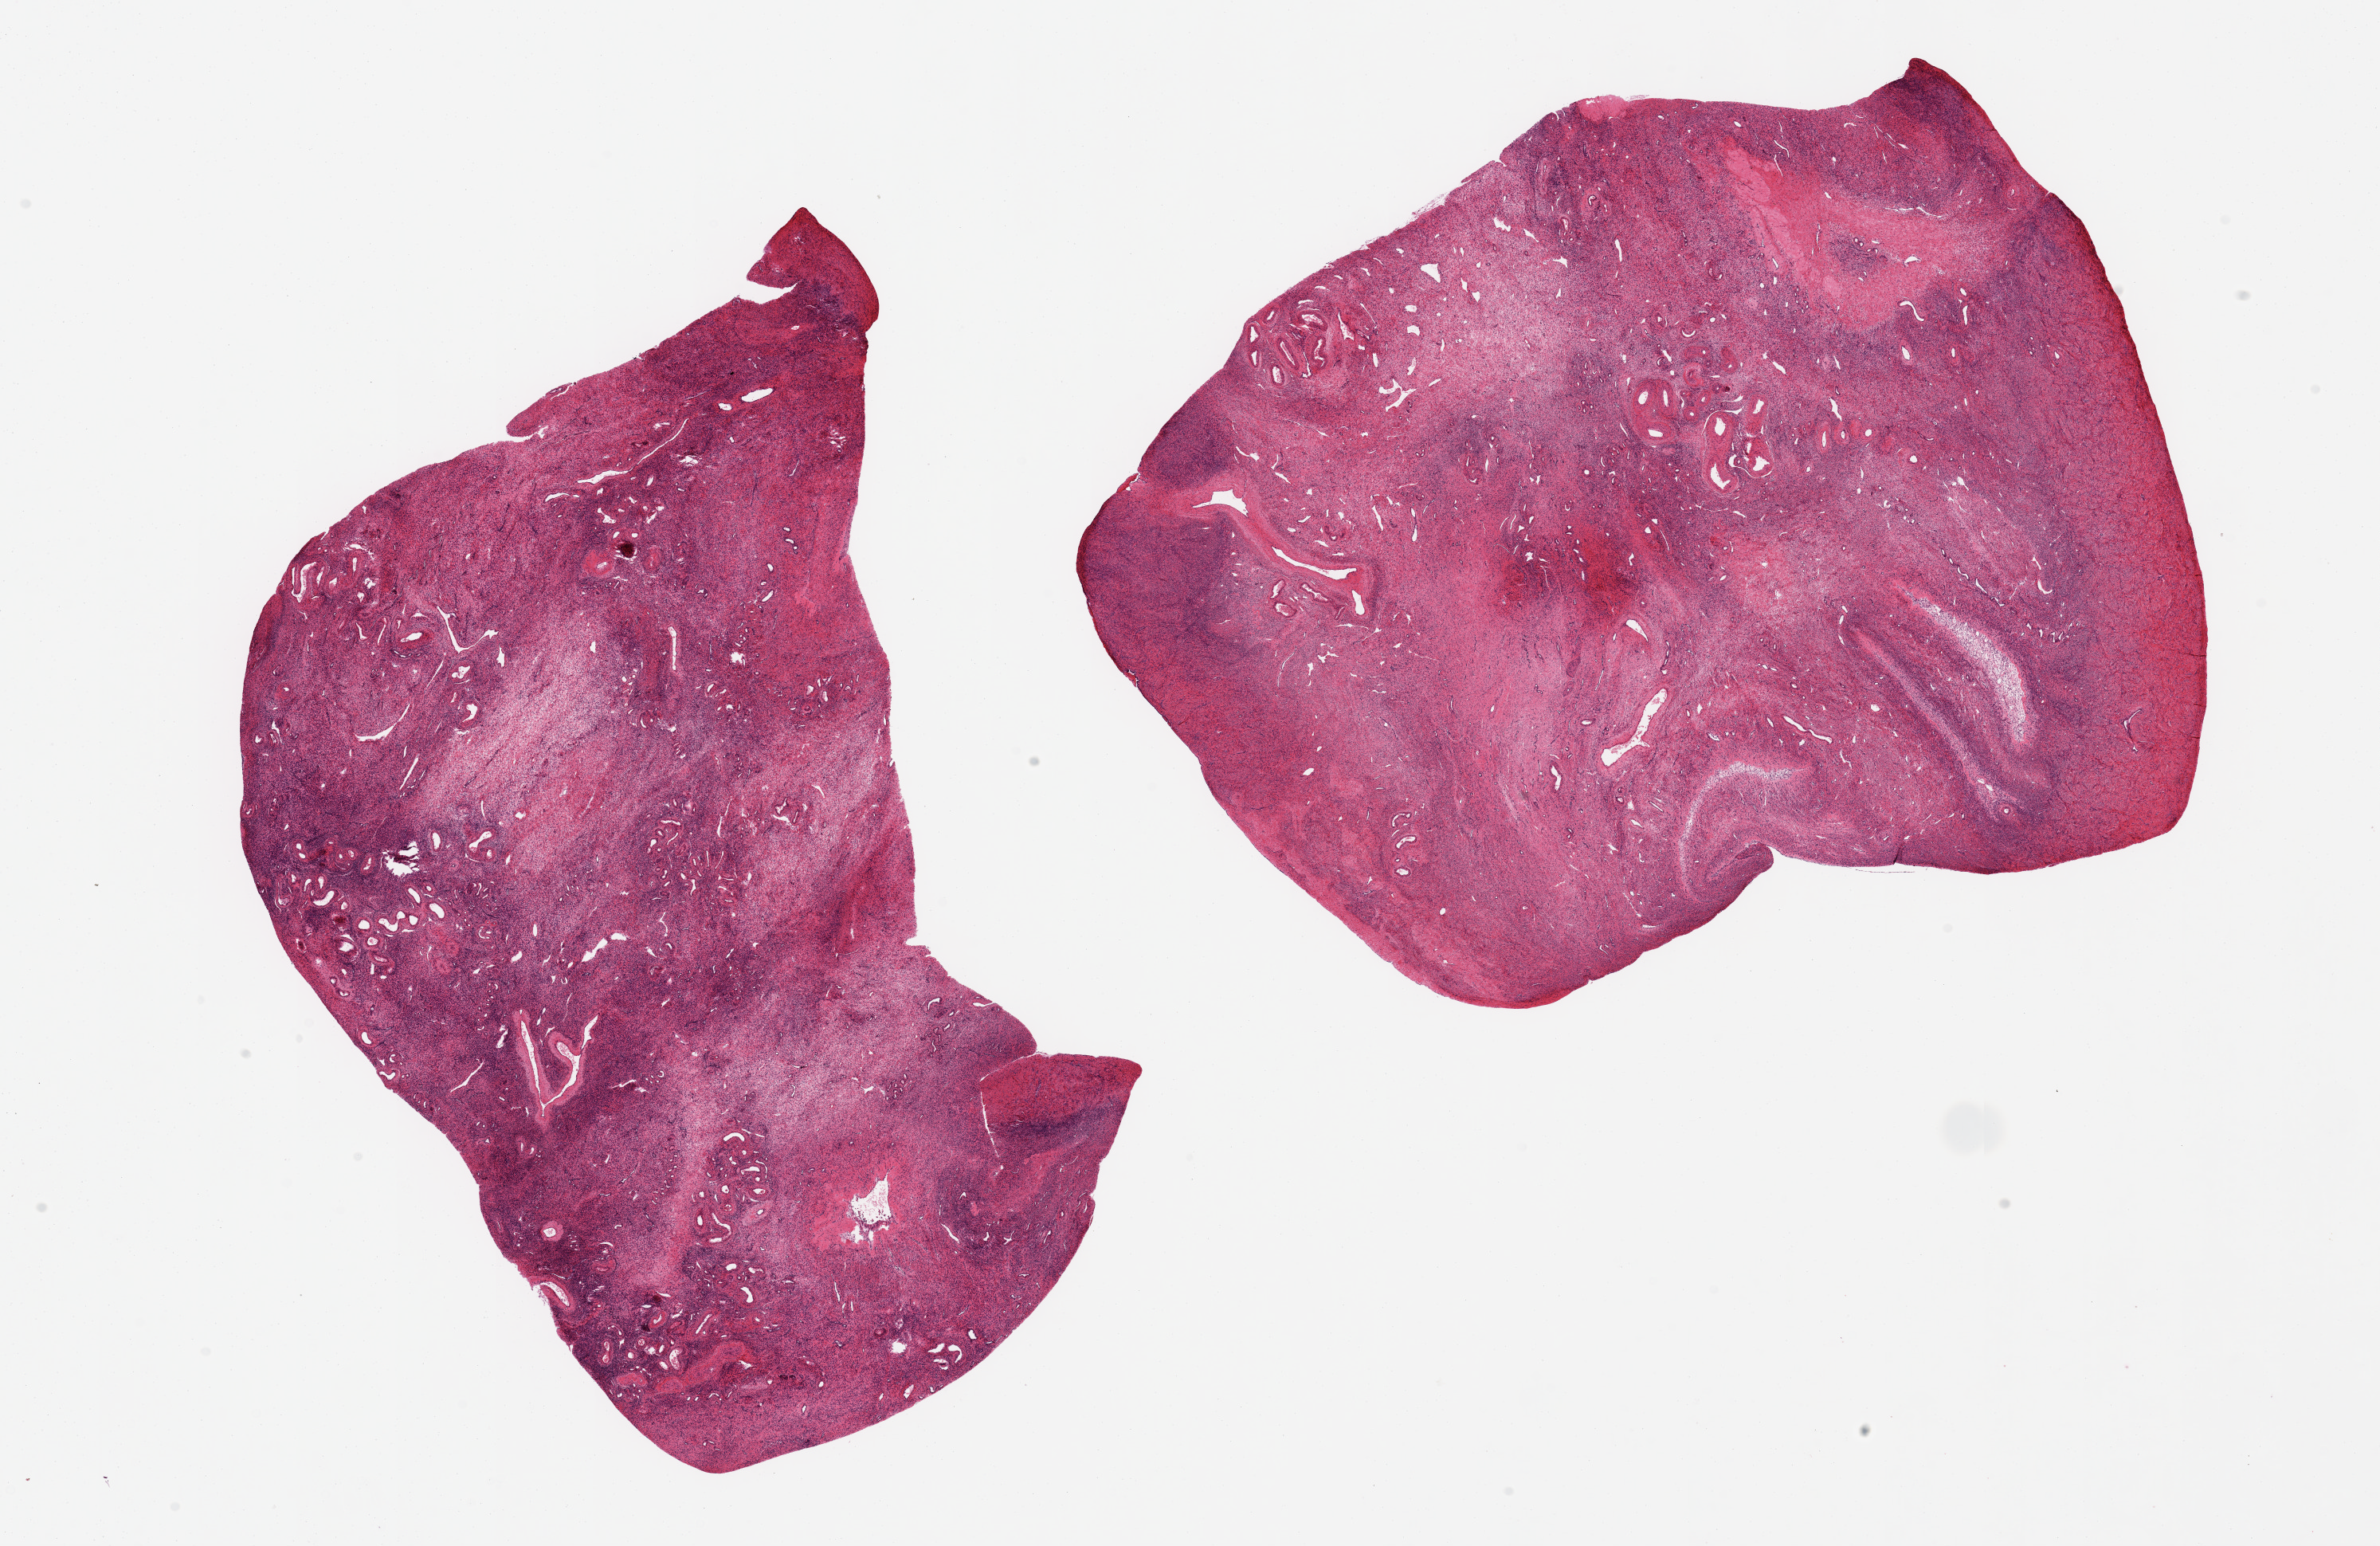
Hematoxylin and eosin (H&E) whole-slide image, low-resolution overview of the scanned area, about 23.6 x 15.3 mm; PAXgene-fixed paraffin-embedded (PFPE) section; sampled site (target tissue): ovary; donor tissue sample. Donor: female.
Review note (as recorded): 2 pieces 10x9 & 10x8 mm; atrophic, no ova, old corpora.